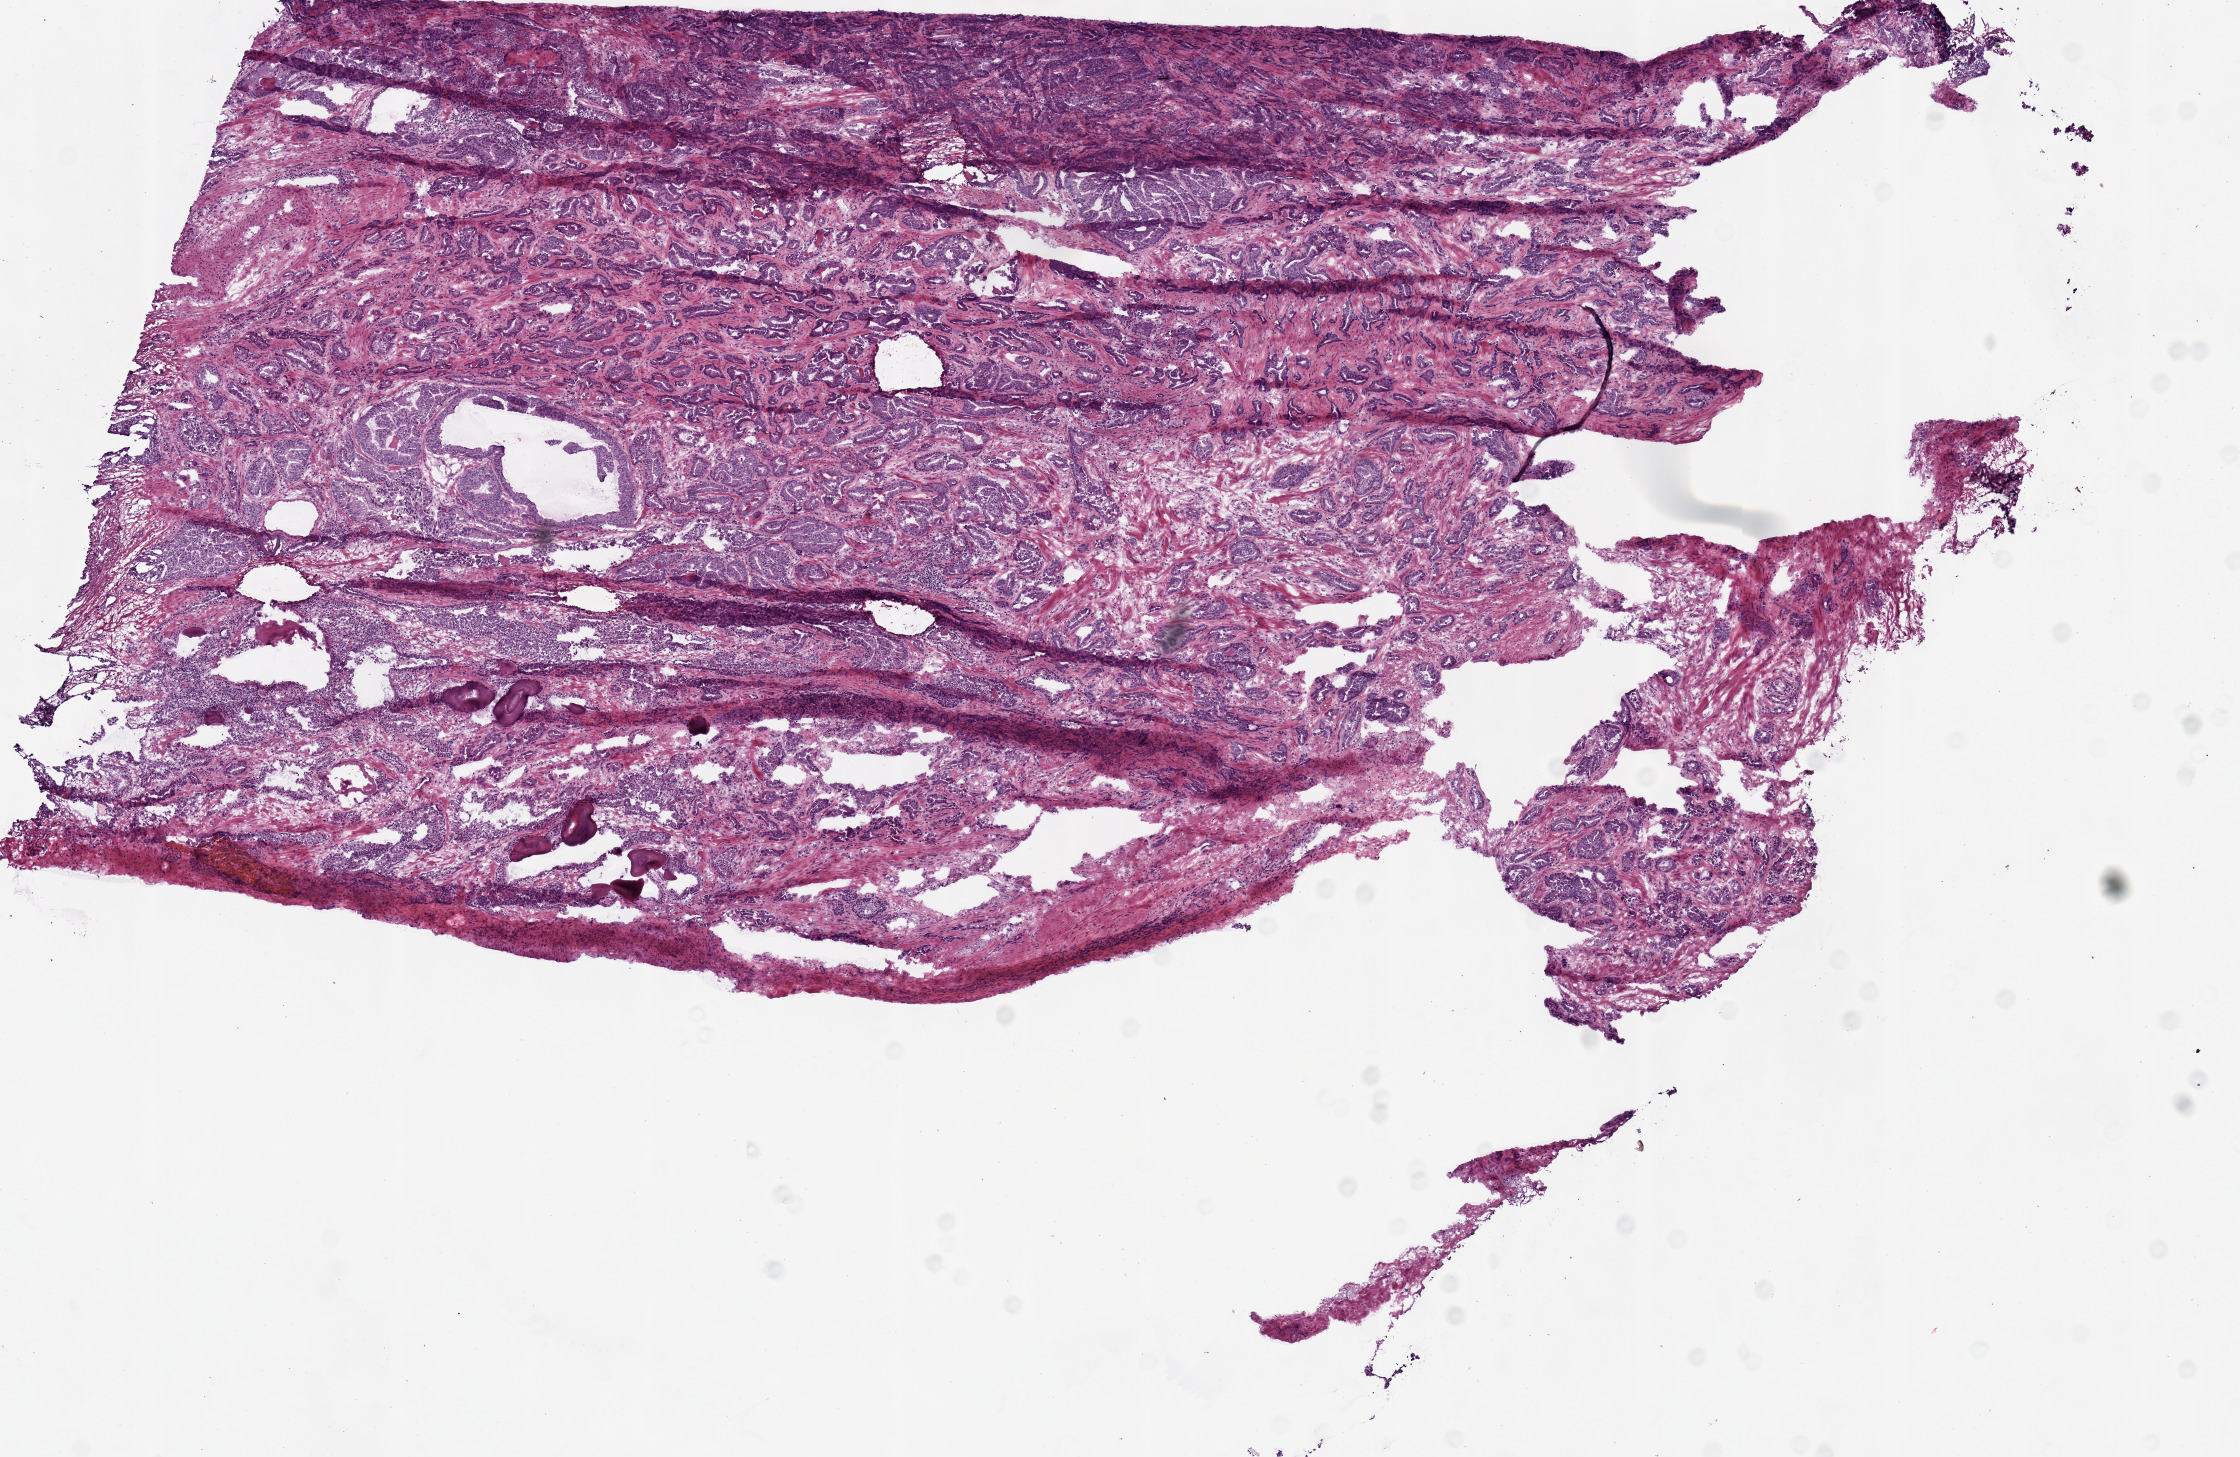
Digitized H&E-stained tissue section (whole slide), a low-resolution overview of the entire scanned area, about 8.9 x 5.8 mm; frozen section; sample: primary tumour, prostate. Male, age 60 years at initial diagnosis. Gleason score: 6 (3+3). Composition of this section per pathologist review: tumour nuclei 70%, necrosis 0%.
Pathologic diagnosis: Acinar cell carcinoma (prostate gland).